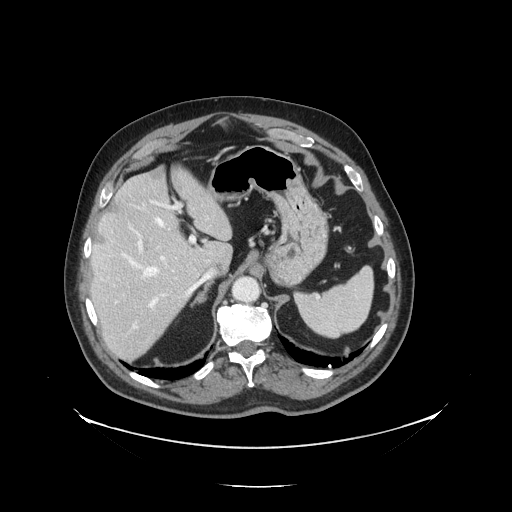
Contrast-enhanced abdominal CT, one axial slice. Slice 96 of 138 in the series (ordered by position). 120 kVp. Intravenous contrast given. Soft-tissue window (W 400 / L 40 HU). 2.5 mm slice thickness. 512 × 512 image matrix. Male patient, age 77 years. Case-level facts recorded for this patient, not image findings: diagnosis: colorectal cancer liver metastases, imaged before liver resection; multiple liver metastases: no; largest metastasis: 1.5 cm.
Annotated regions visible in this slice (manually delineated by an expert):
- hepatic veins: bounding box (x1, y1, x2, y2) in pixels: (124, 217, 210, 296)
- liver: (91, 170, 232, 361)
- planned liver remnant (the part of the liver to remain after resection): (92, 169, 232, 288)
- portal vein (with intrahepatic branches): (116, 202, 194, 308)